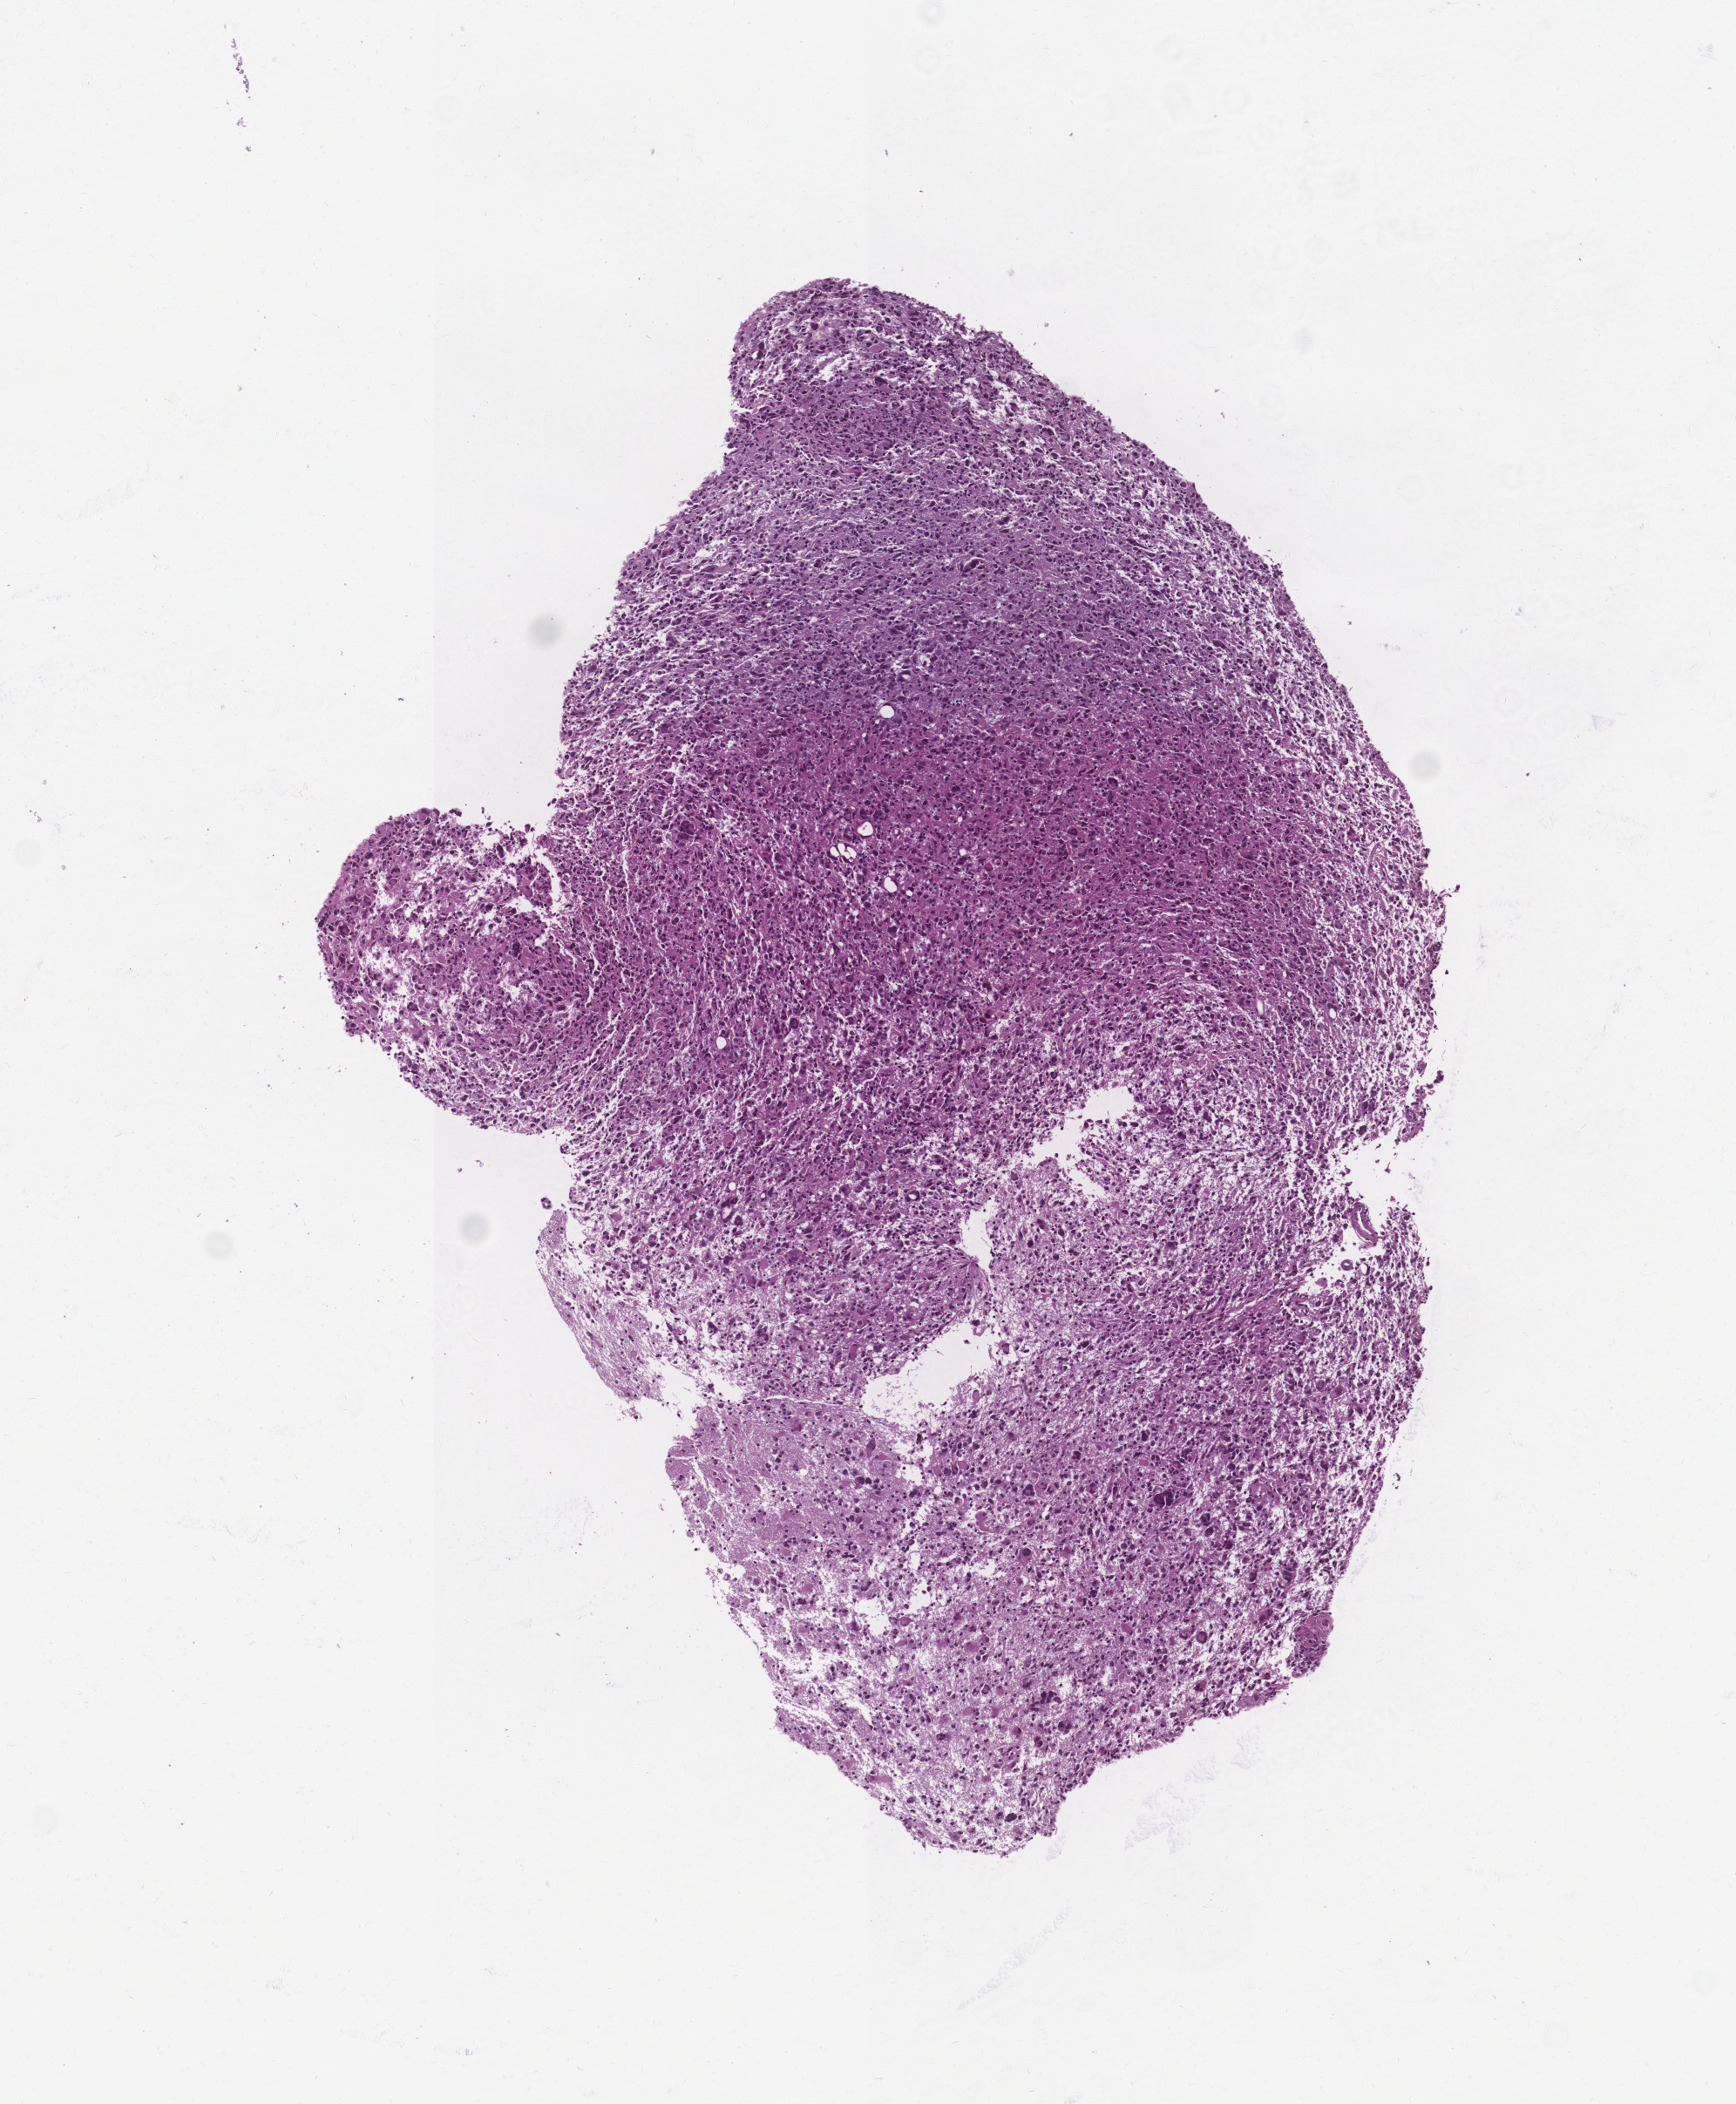
H&E-stained whole-slide image — low-resolution overview of the scanned area, about 4.0 x 4.9 mm (slide scanned at 20x); tumour tissue sample, sampled site: brain. Patient: male, age 71 years. Pathologist review of this section (percent, as recorded): tumour nuclei 80%, necrosis 7%.
Histologic diagnosis: Glioblastoma. Primary tumour site (as recorded): temporal lobe.